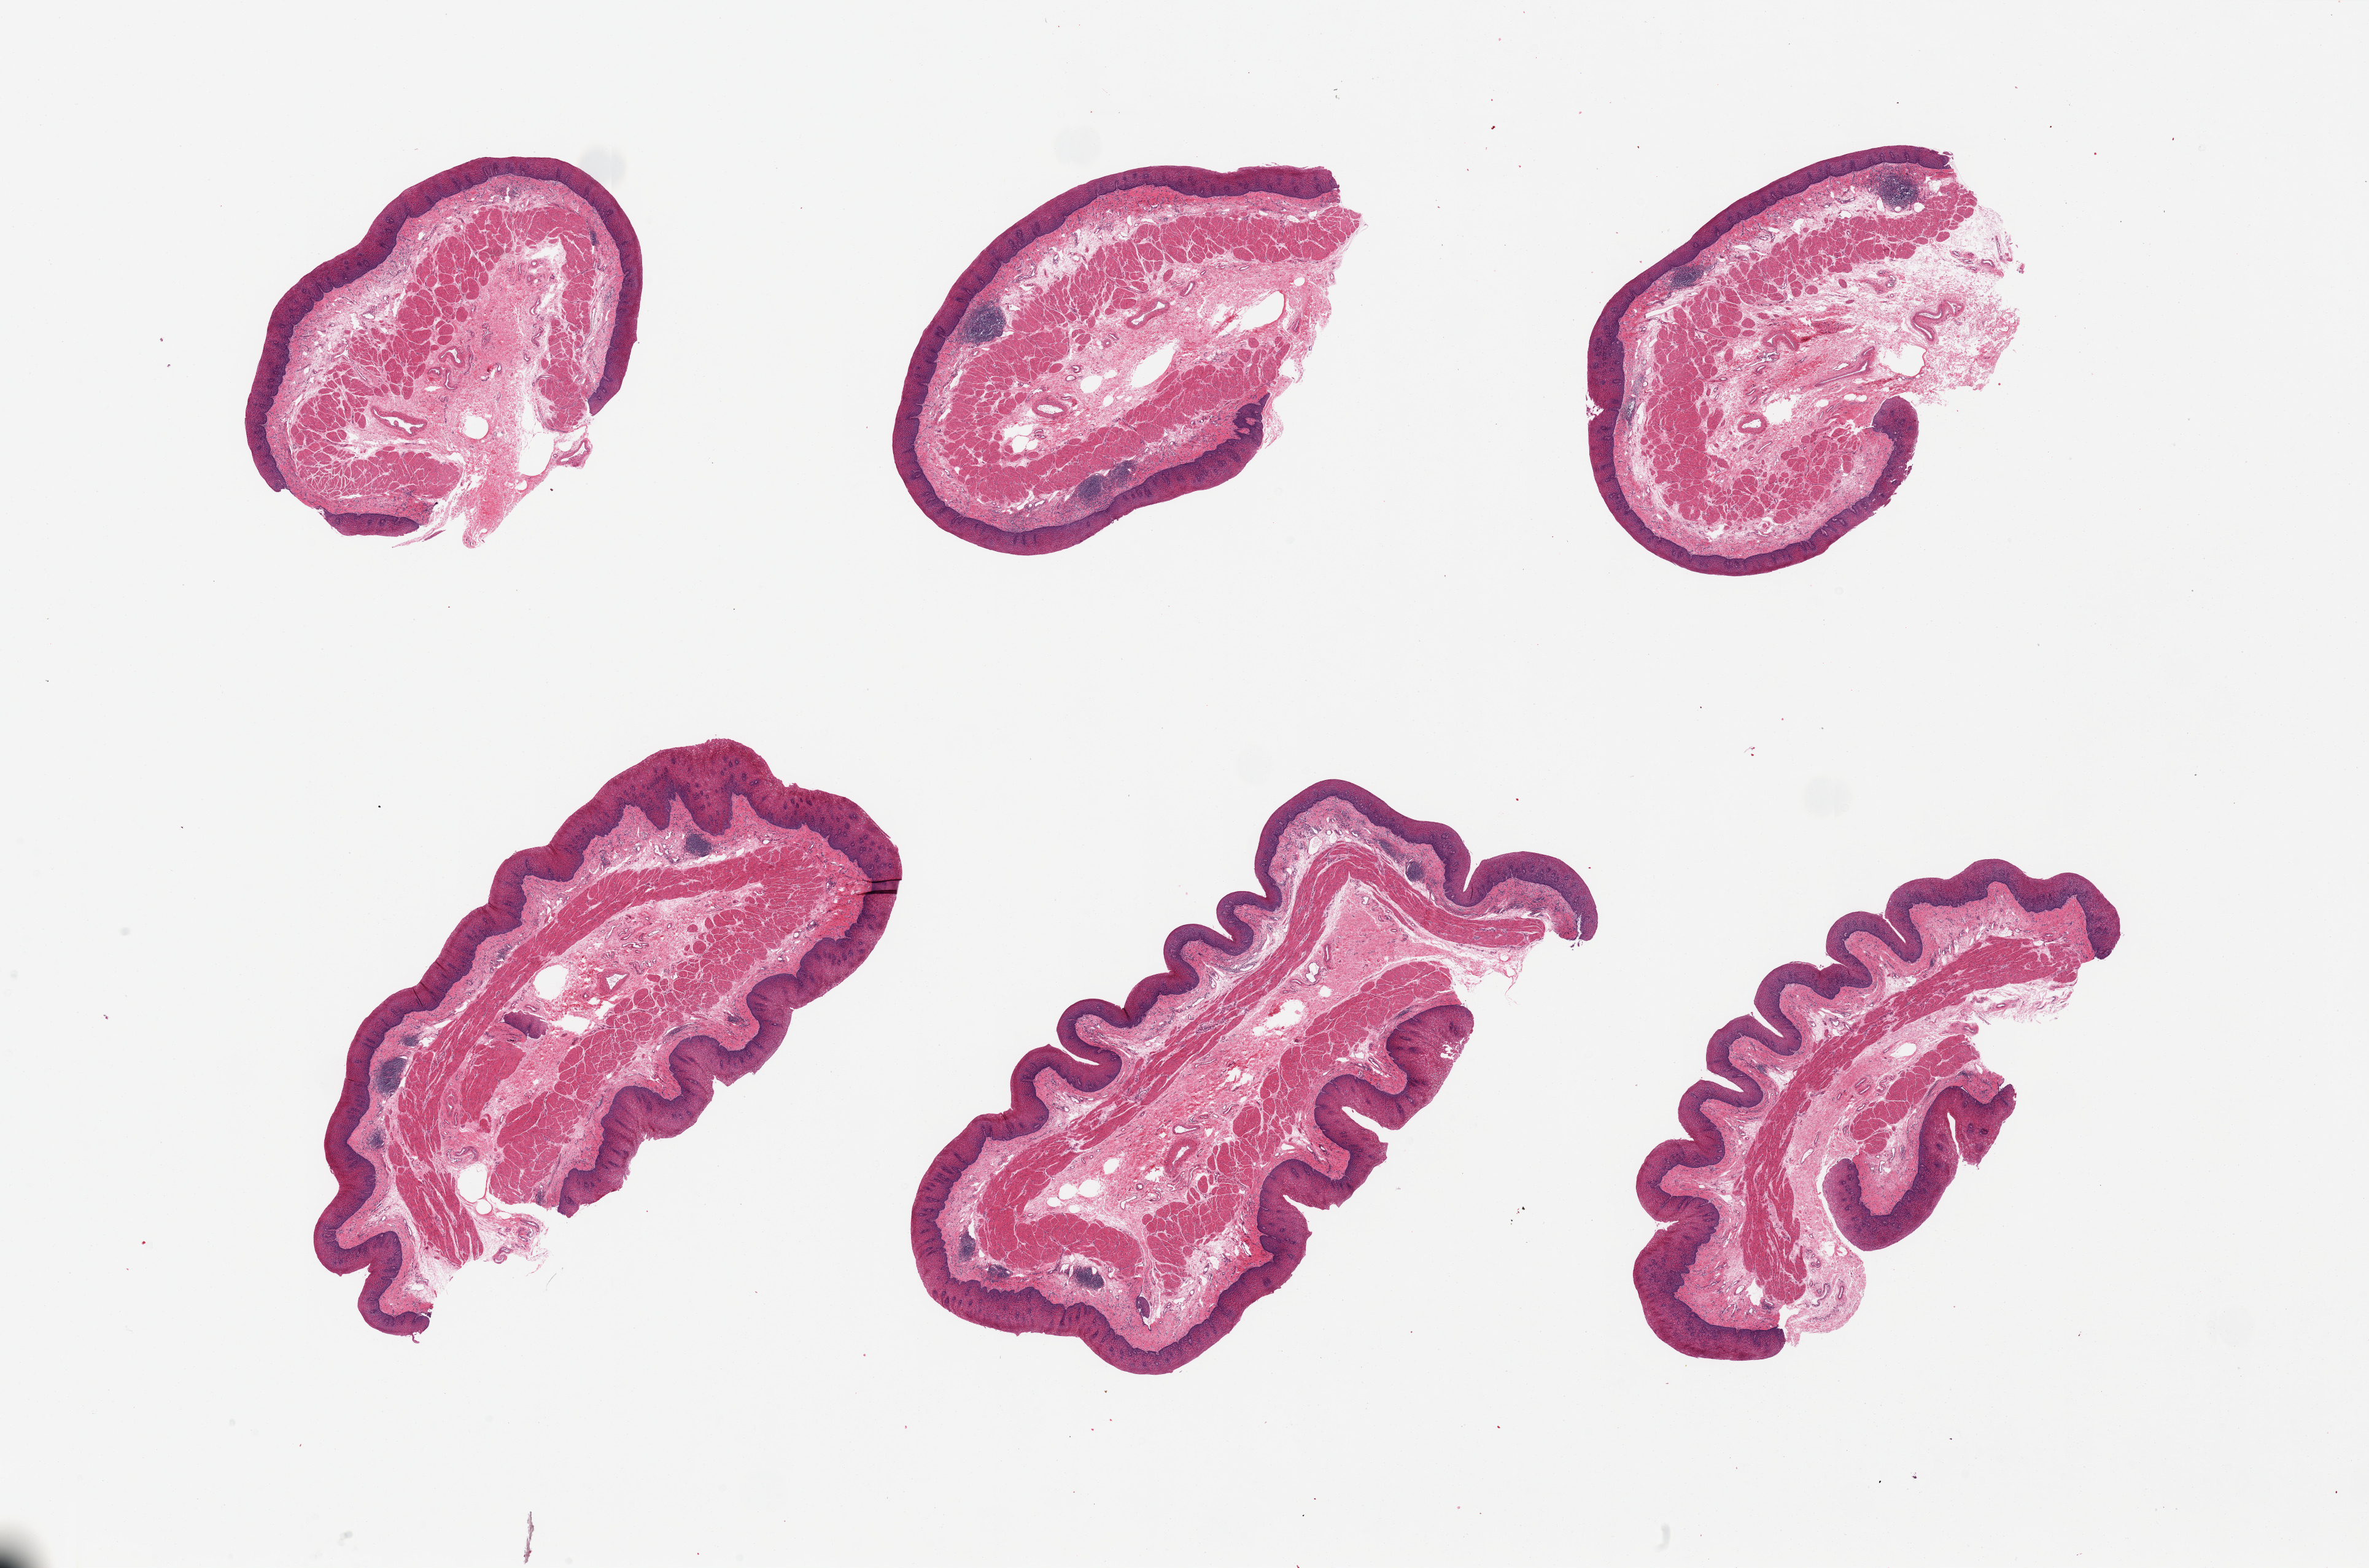
Digitized haematoxylin and eosin-stained section, whole scanned area (about 30.5 x 20.2 mm, slide scanned at 20x) shown as a low-resolution overview. PAXgene-fixed, paraffin-embedded tissue. Section of esophageal mucous membrane (target tissue). Donor tissue sample. Female donor.
Pathologist's review note for this sample: 6 pieces; well preserved, well dissected.